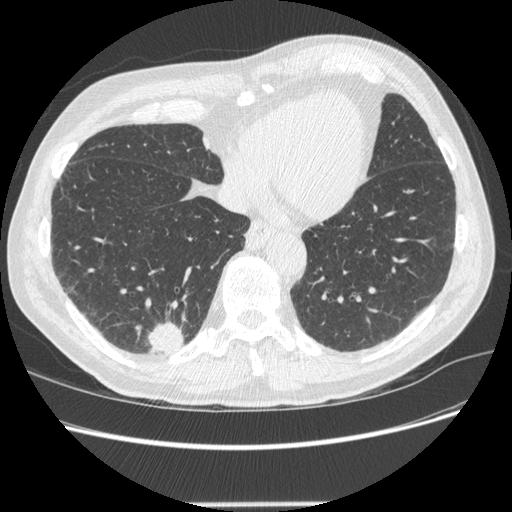
Low-dose screening chest CT, one axial slice; slice 68 of 245 in the series (ordered by position); reconstruction kernel STANDARD; 120 kVp; lung window (W 1500 / L -600 HU); 512 × 512 image matrix.
Annotated regions visible in this slice (expert manual segmentation):
- lesion 1 (tumor, lower lobe of right lung): bounding box <148,322,184,354> (left, top, right, bottom; pixels)